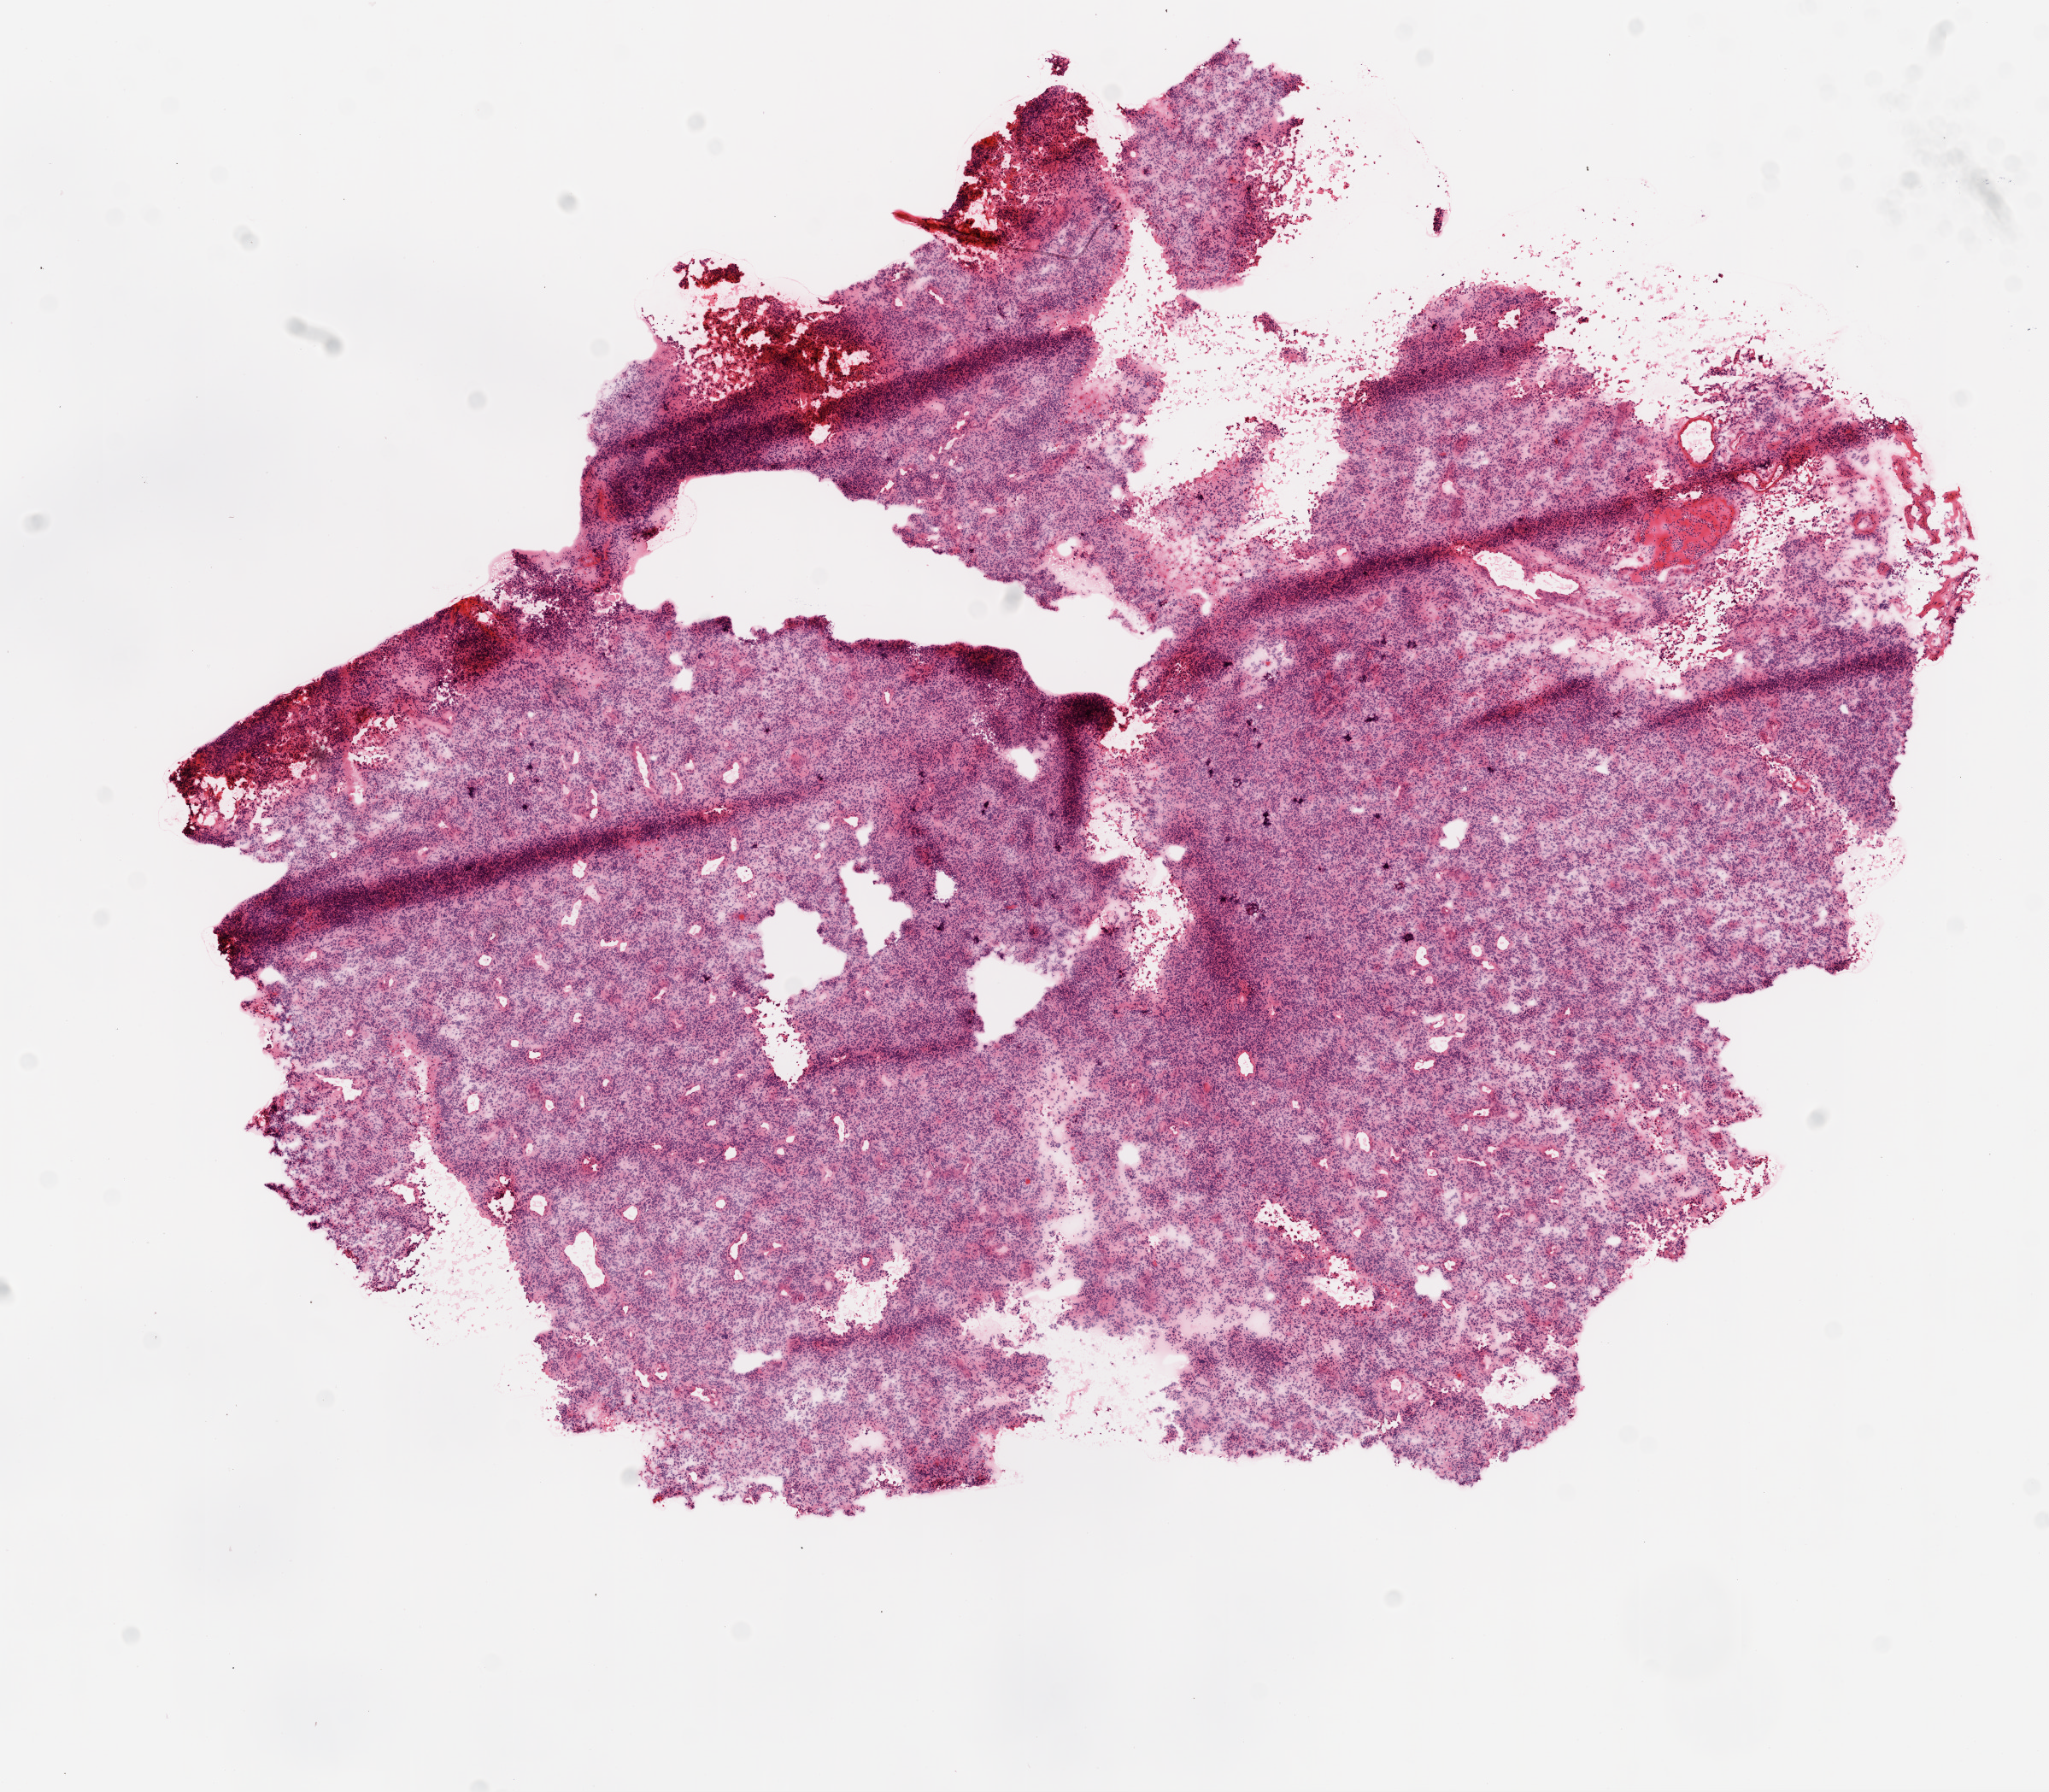
Digitized H&E tissue section (whole slide) — shown as a low-resolution overview of the whole scanned area (about 9.7 x 8.5 mm, acquisition: 20x scan). Frozen section from the bottom of the tissue portion. Primary tumour sample from the brain. Patient: female, age at initial diagnosis 31 years. Pathologist review of this section (percent, as recorded): tumour cells 98%, tumour nuclei 95%, normal cells 0%, stromal cells 0%, necrosis 2%.
- pathologic diagnosis: Glioblastoma